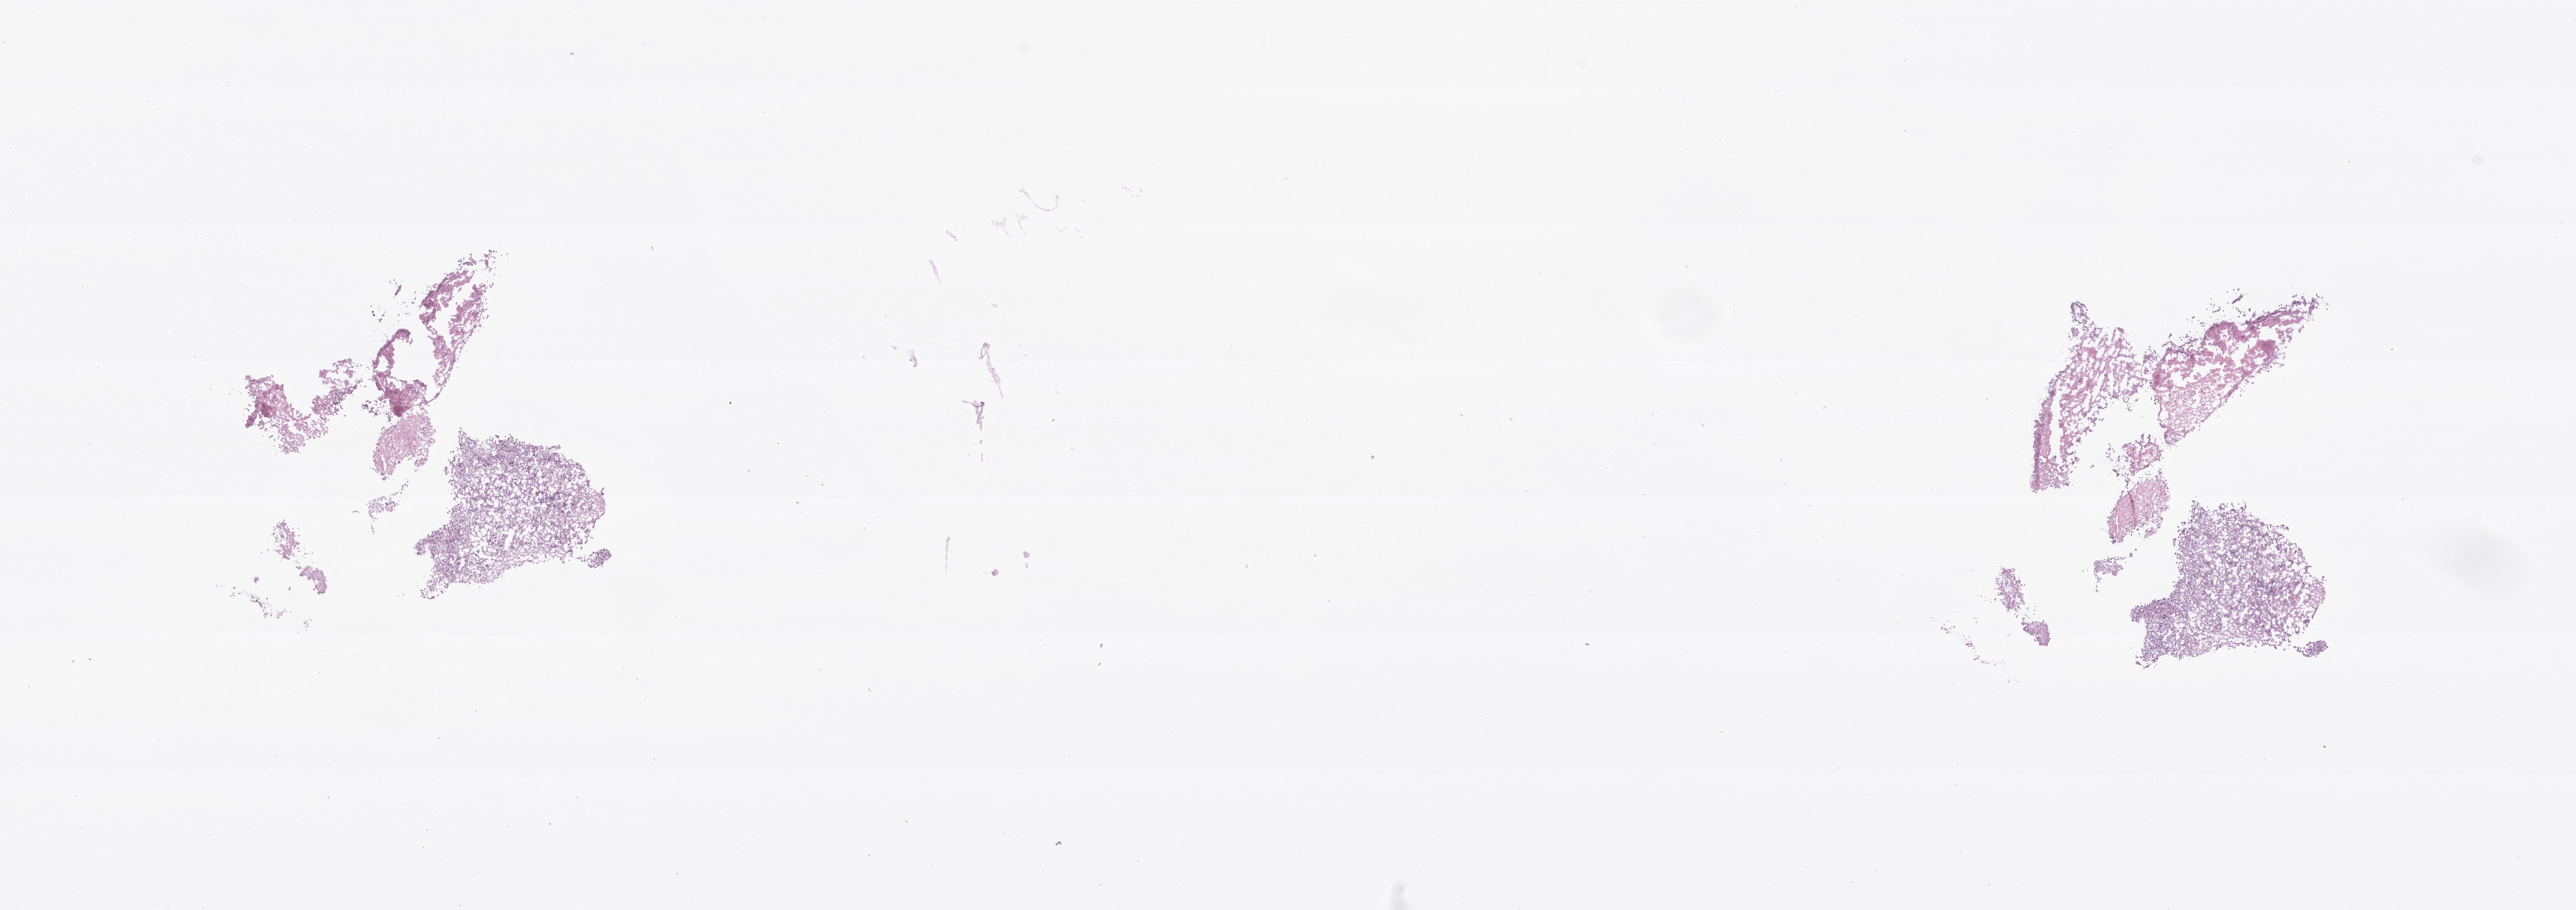
Digitized hematoxylin and eosin (H&E)-stained section of tumor tissue from the parietal lobe, a low-resolution overview of the entire scanned area, about 20.0 x 7.1 mm, frozen section (OCT-embedded). Patient female; age 45 months (3 years 9 months).
Recorded diagnosis: Astroblastoma.